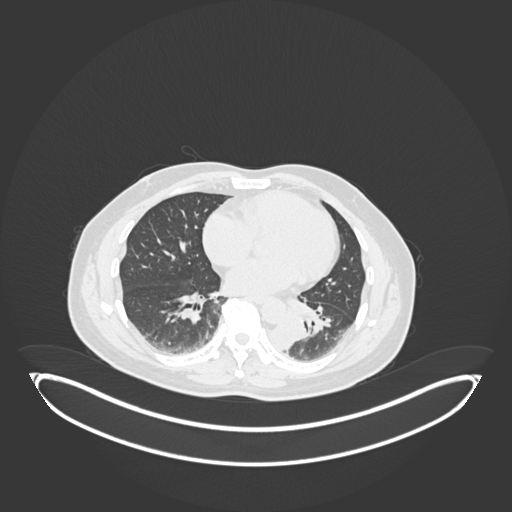
Chest CT, one axial slice; position 74 of 258 along the scan axis; lung window (W 1500 / L -600 HU); 512 × 512 image matrix, field of view 500 × 500 mm. Patient: male, 54 years. From the clinical record (not read from this slice): clinical TNM (as recorded): T3 N0 M0.
Annotated regions visible in this slice (bounding box drawn by a radiologist):
- lung tumour (recorded histology: squamous cell carcinoma): bounding box (x1, y1, x2, y2) in pixels: (269, 304, 308, 350)